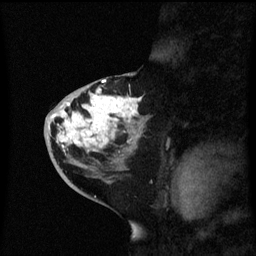
Breast MRI (dynamic contrast-enhanced), one sagittal slice. Position 30 of 60 along the scan axis. Dynamic contrast-enhanced series, image 2 of 3 at this slice position (ordered by acquisition). 1.5 T. TE 4.2 ms, TR 8.4 ms. 2.3 mm slice thickness. 256 × 256 image matrix, field of view 200 × 200 mm. Patient: female, 46 years. Case-level facts recorded for this patient, not image findings: setting: breast cancer imaged before/during neoadjuvant chemotherapy; receptor status: HER2-positive.
Structures marked on this image (semi-automatic segmentation, software-assisted and operator-edited):
- analysis volume of interest (the breast-tissue region the enhancement analysis was run in; not a lesion): bounding box <44,86,153,171> (left, top, right, bottom; pixels)
- tumour enhancement mask (voxels above the 70 % enhancement threshold inside the analysis volume of interest): <52,90,141,151>